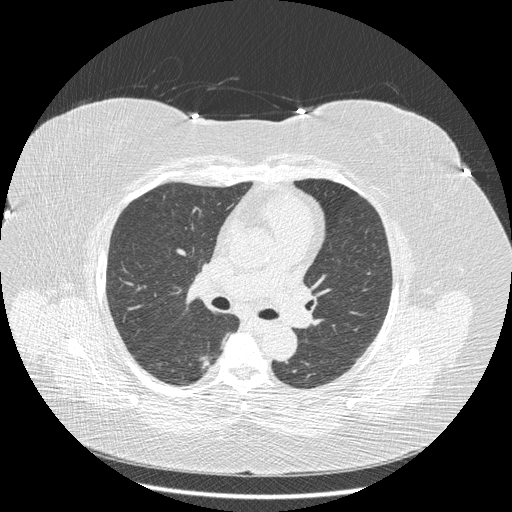
Chest CT (low-dose screening protocol), one axial image, baseline annual screen, lung window (W 1500 / L -600 HU), 1.25 mm slice thickness. Female, age 58 years at enrolment.
Lesion marked by an expert reader, bounding box [x1, y1, x2, y2] px = [185, 342, 227, 382]. Reader record for this screening exam (exam-level; its link to the box is not recorded): non-calcified nodule or mass ≥4 mm, right lower lobe, 15 × 10 mm, smooth margins, soft tissue attenuation. Official screen result: positive, change unspecified: nodule(s) >= 4 mm or enlarging nodule(s), mass(es), or other non-specific abnormalities suspicious for lung cancer.